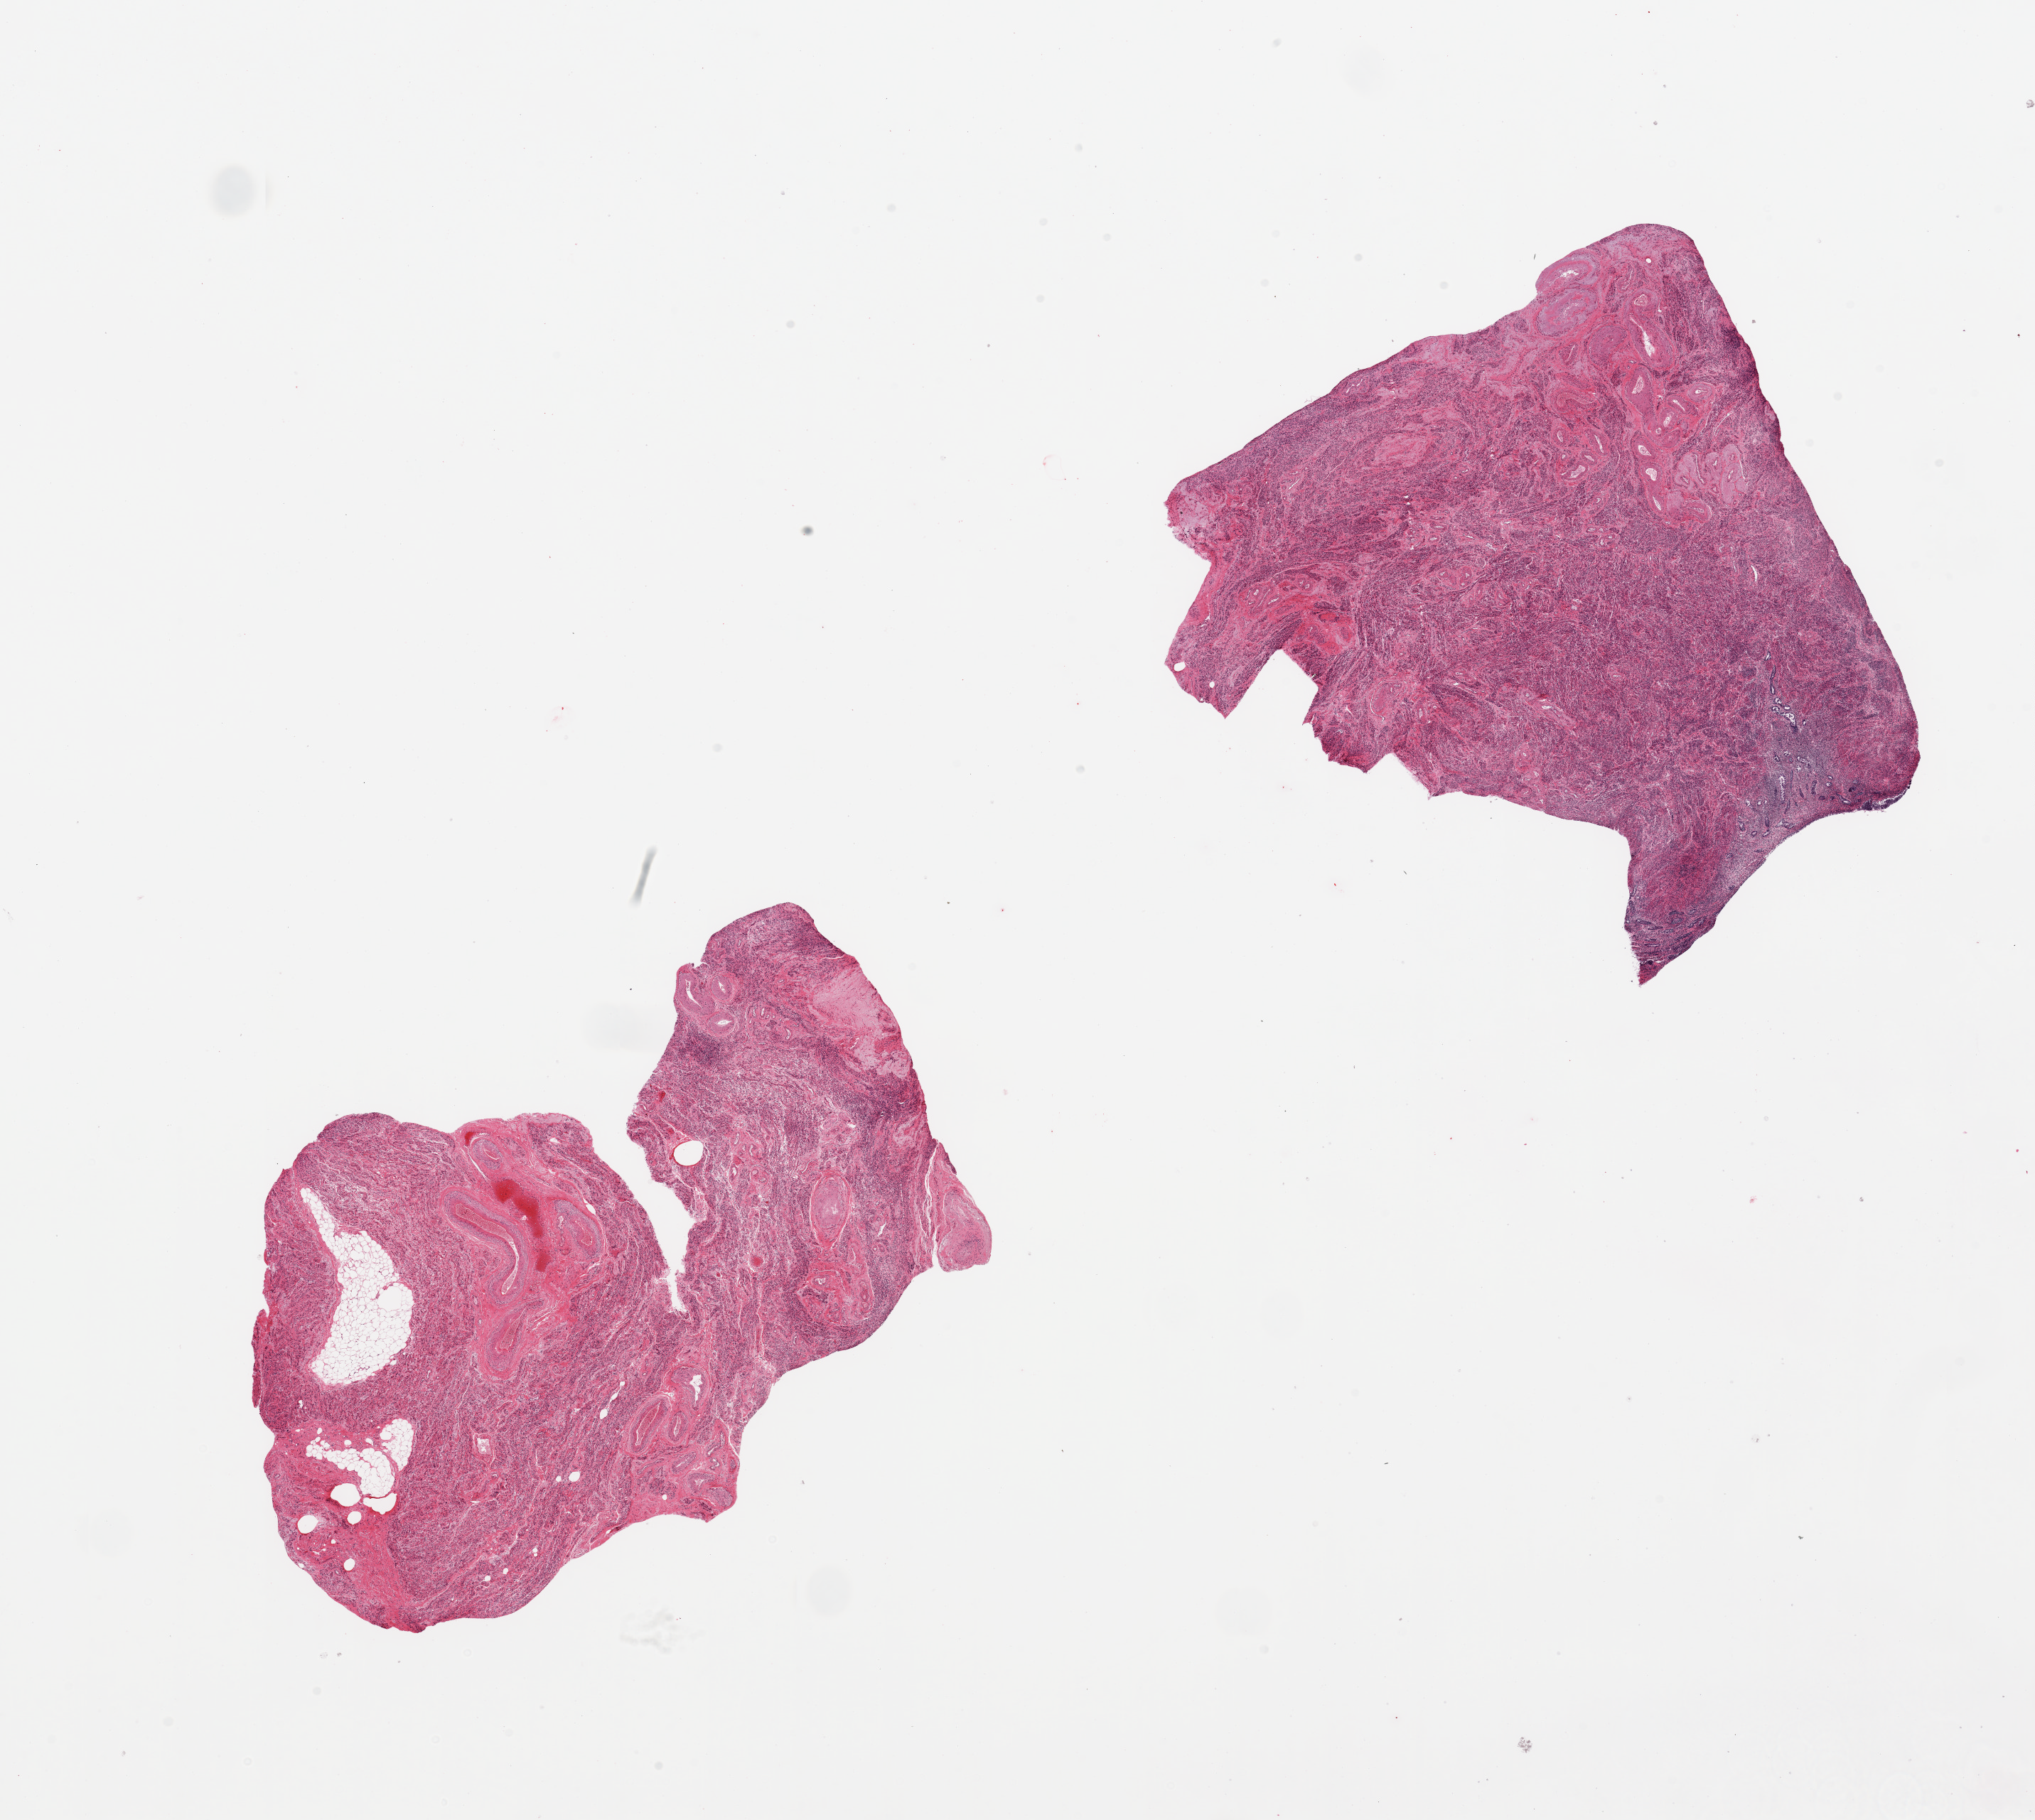
Haematoxylin and eosin whole-slide image — whole scanned area (about 22.6 x 20.3 mm, acquisition: 20x scan) shown as a low-resolution overview; PAXgene-fixed paraffin-embedded (PFPE) section; sampled site (target tissue): uterus; tissue donor sample. Female donor.
Review note (as recorded): 6 pieces, one piece is myometrium with atrophic endometrium, one piece is largely vessels/fat.